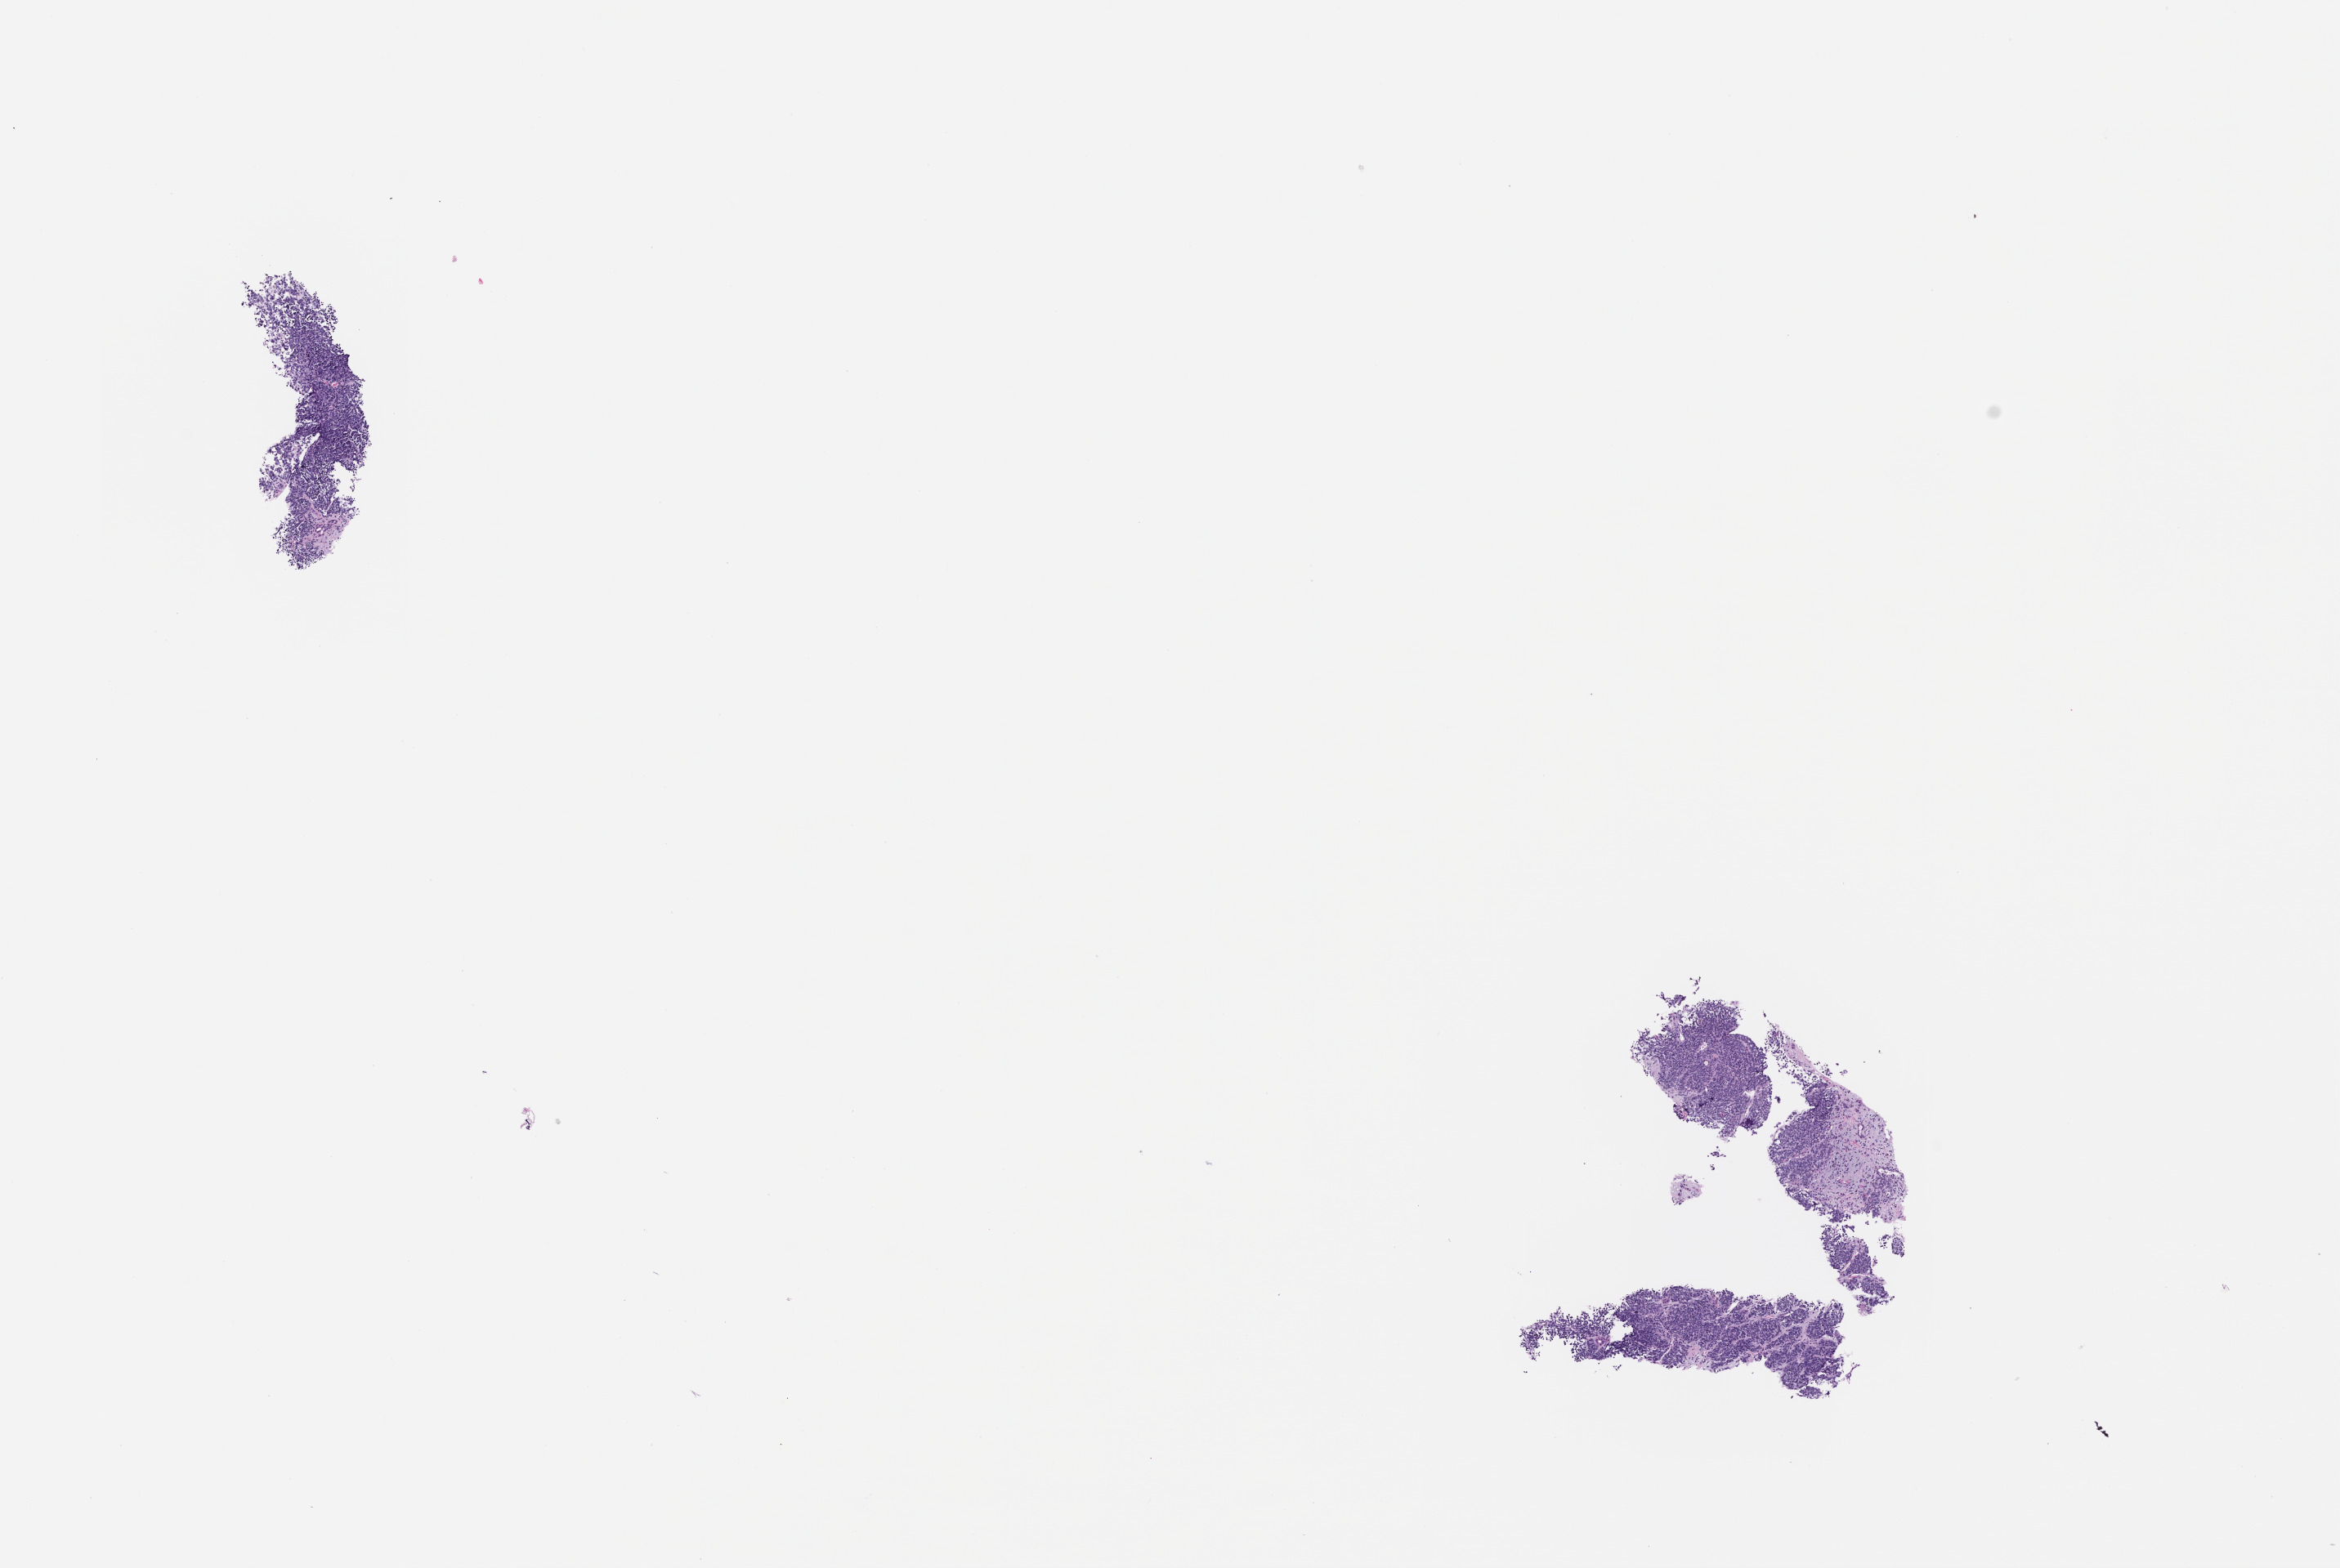
Hematoxylin and eosin (H&E) whole-slide image — shown as a low-resolution overview of the whole scanned area (about 11.6 x 7.7 mm), formalin-fixed, paraffin-embedded (FFPE) tissue, specimen time point: collected at baseline (before treatment). Patient sex: male.
This section: metastasis (sampled organ not recorded). Primary diagnosis of the patient: Small Cell Lung Carcinoma.